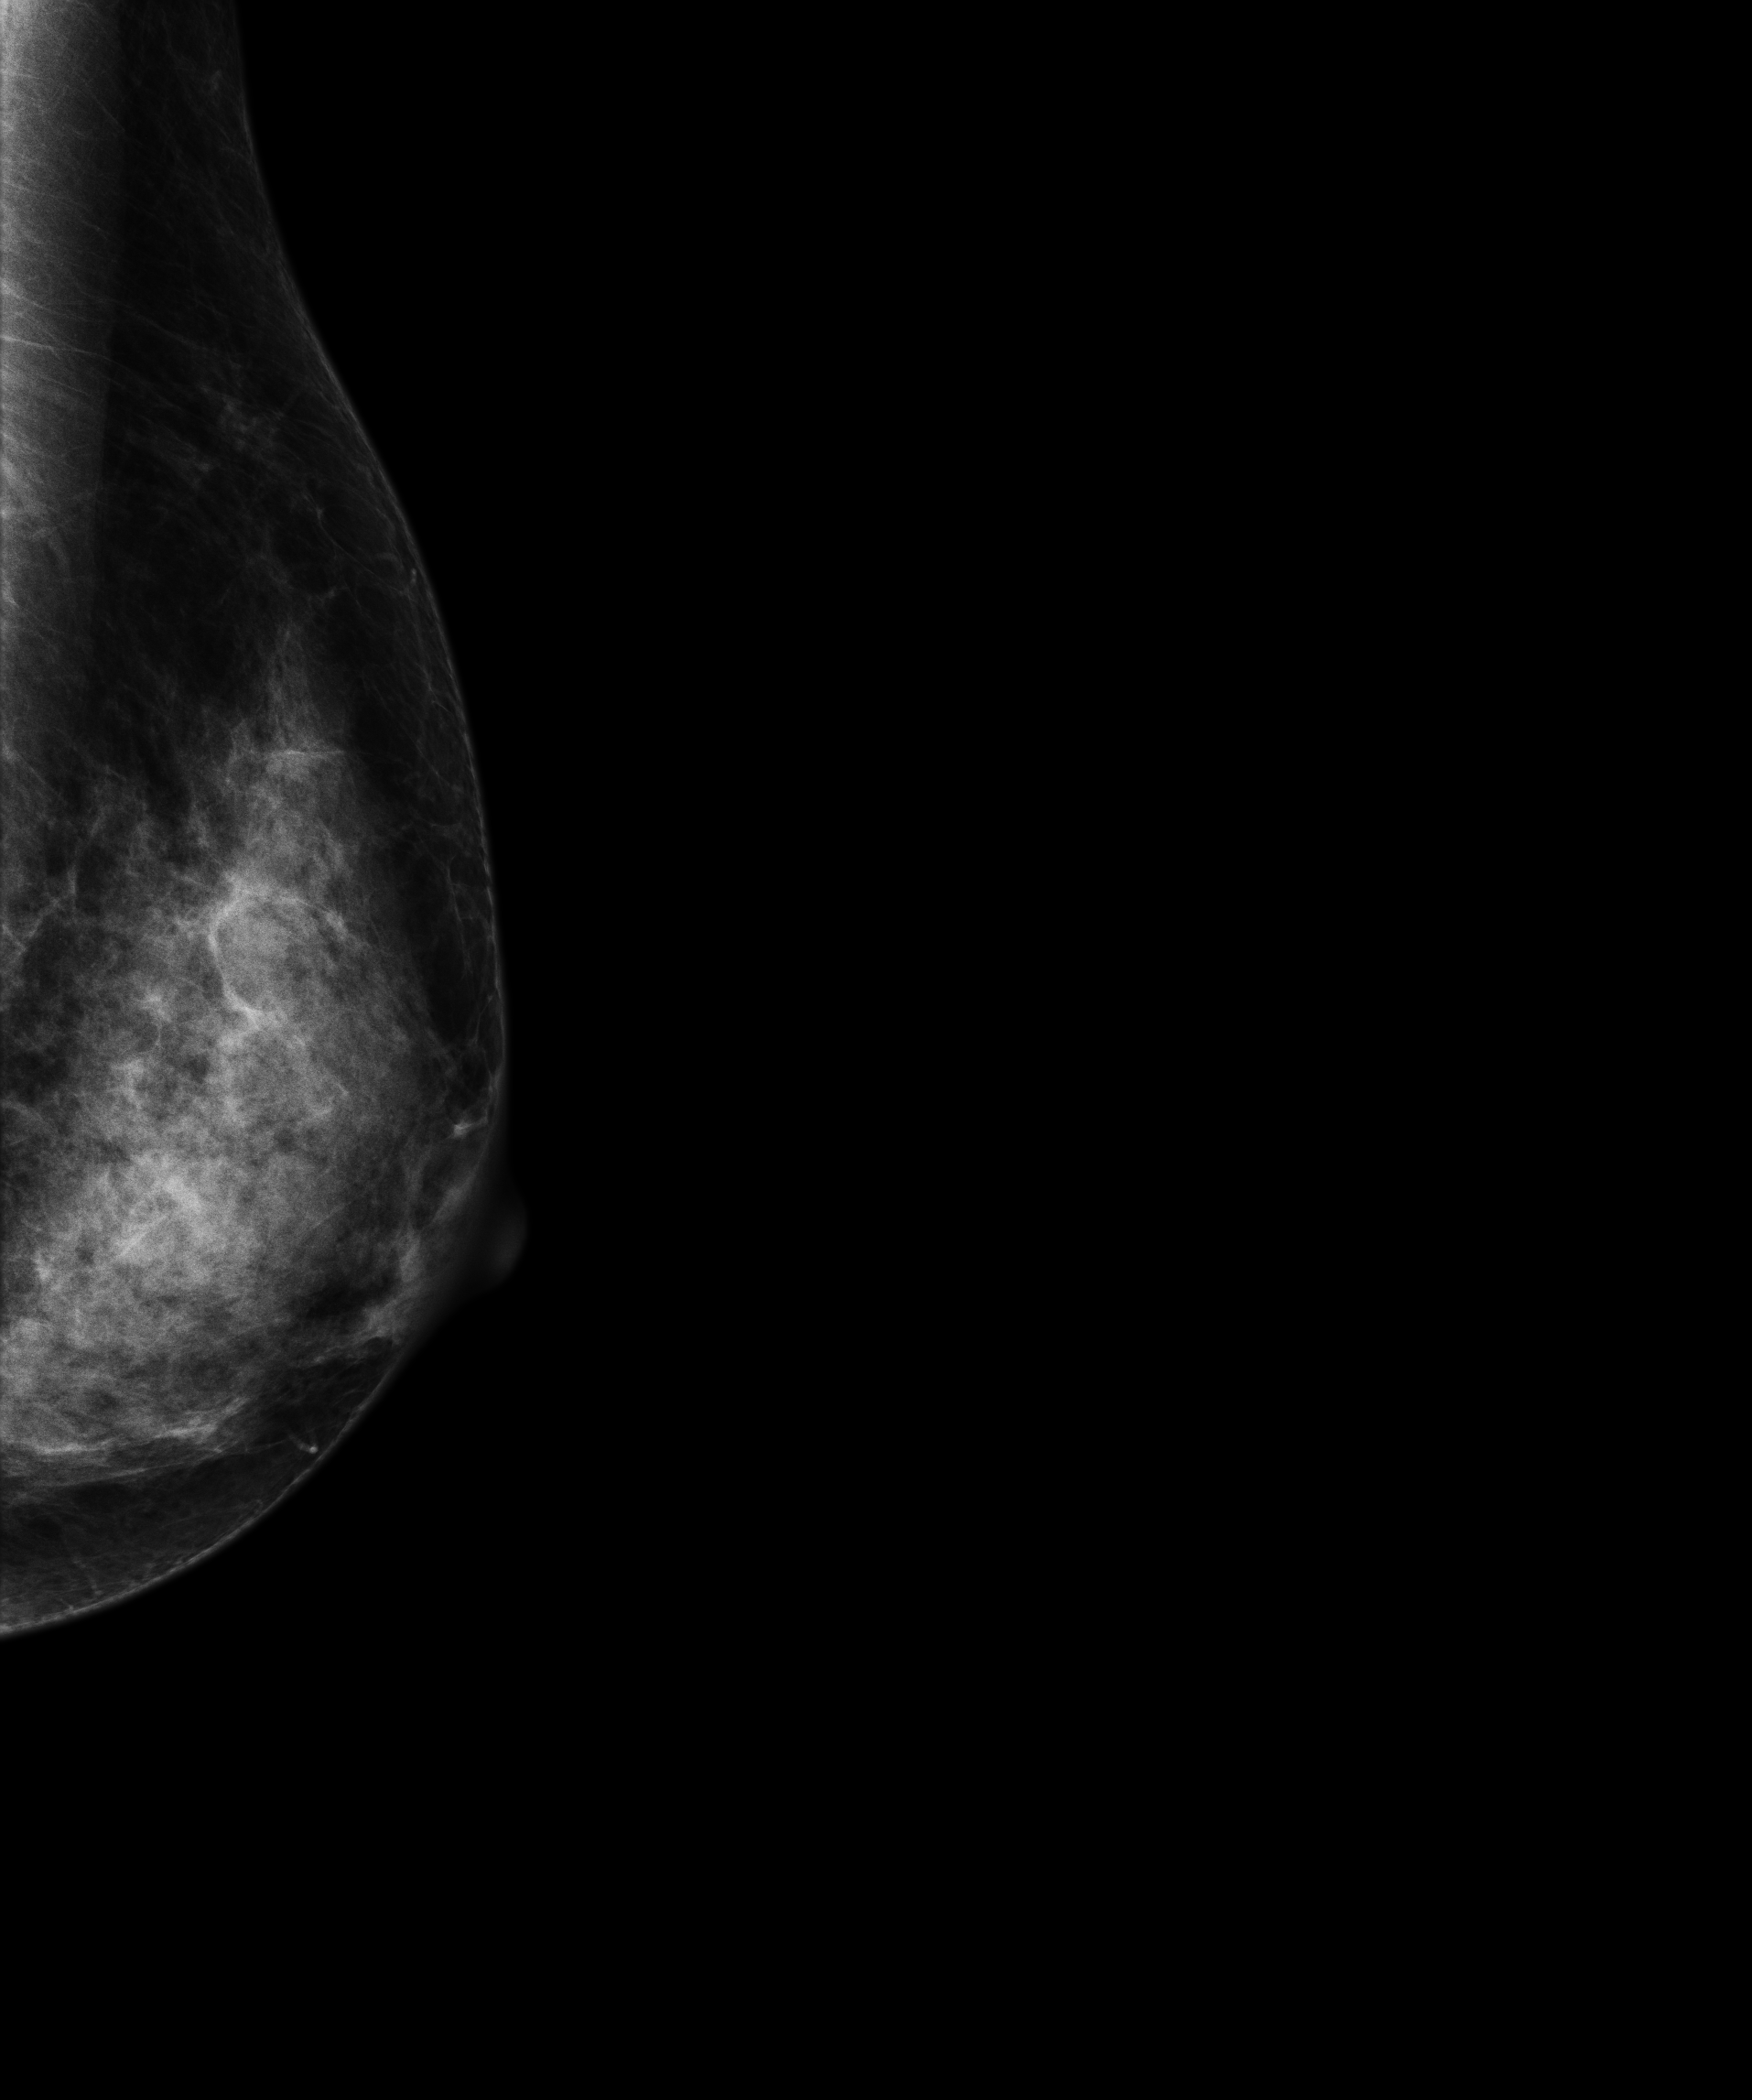
Screening examination. Patient: female, 55 years.
Image type: full-field digital mammogram. Breast: left. Projection: laterally exaggerated craniocaudal (XCCL) view.